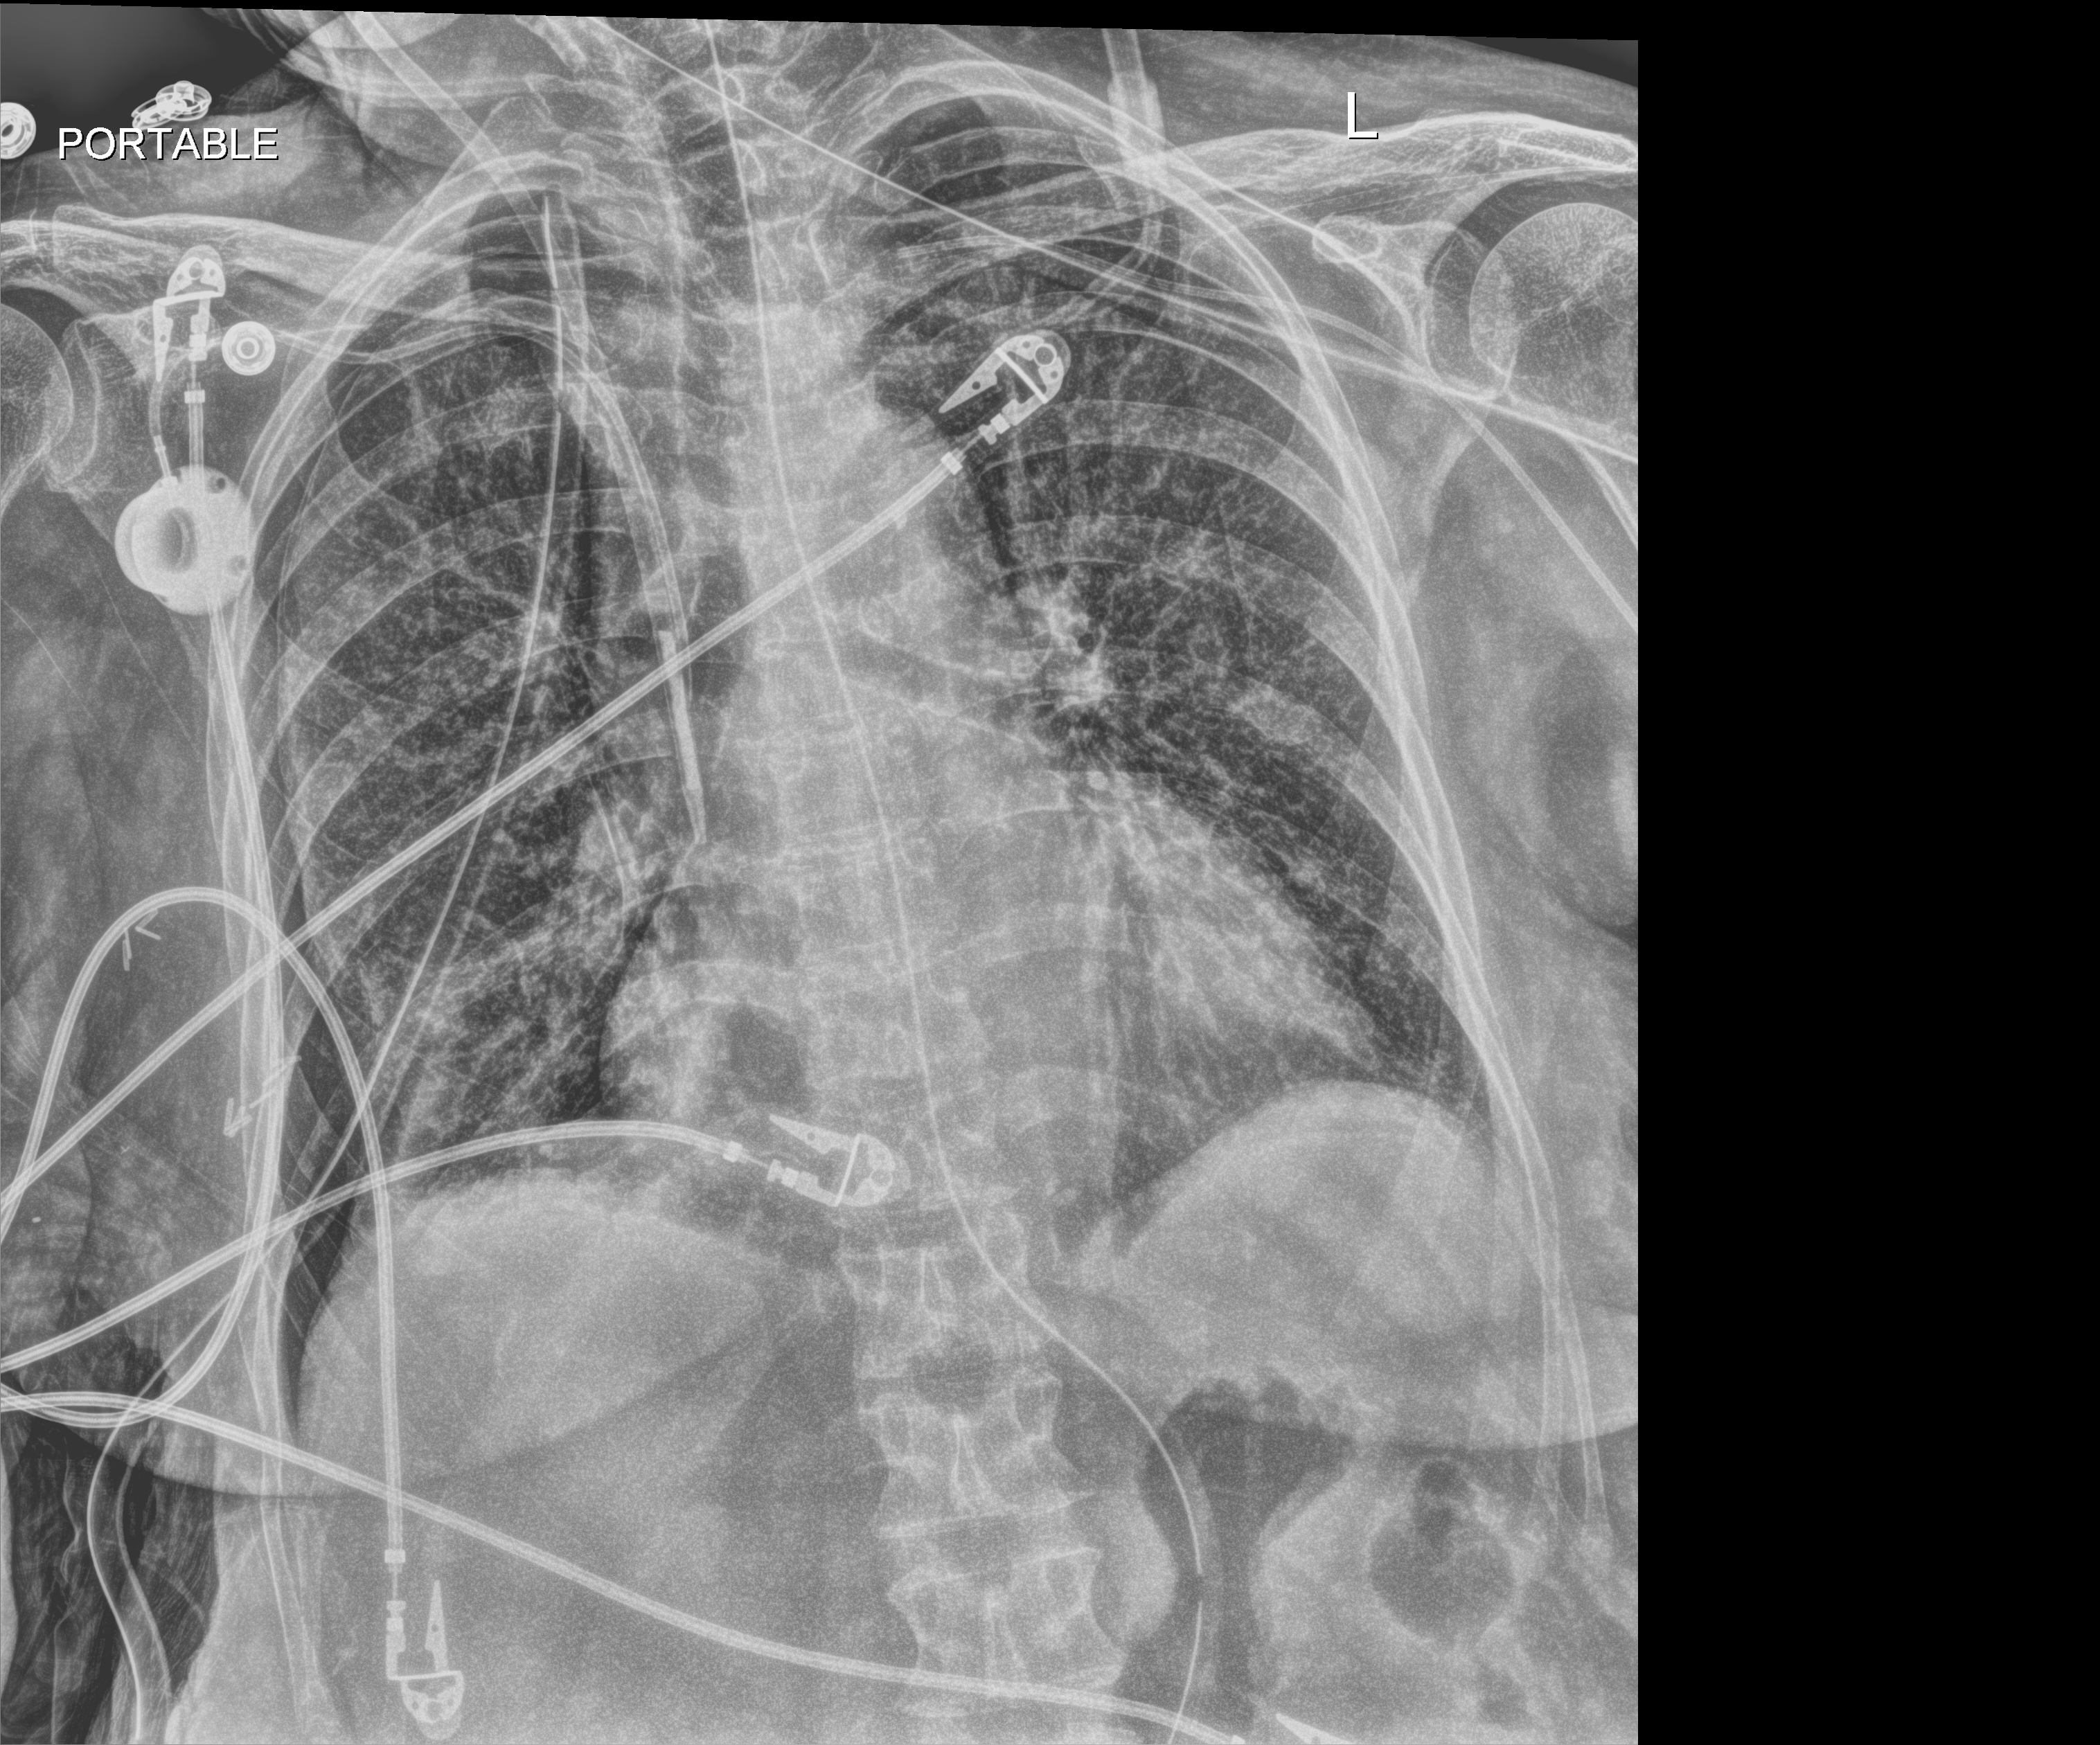
Chest X-ray, anteroposterior (AP) projection. Female patient hospitalised with COVID-19, age 60–74 years.
Admission-level facts for this patient (not findings on this image; timing relative to this image not recorded):
- diabetes (admission record): no
- admitted to intensive care during this hospital stay: yes